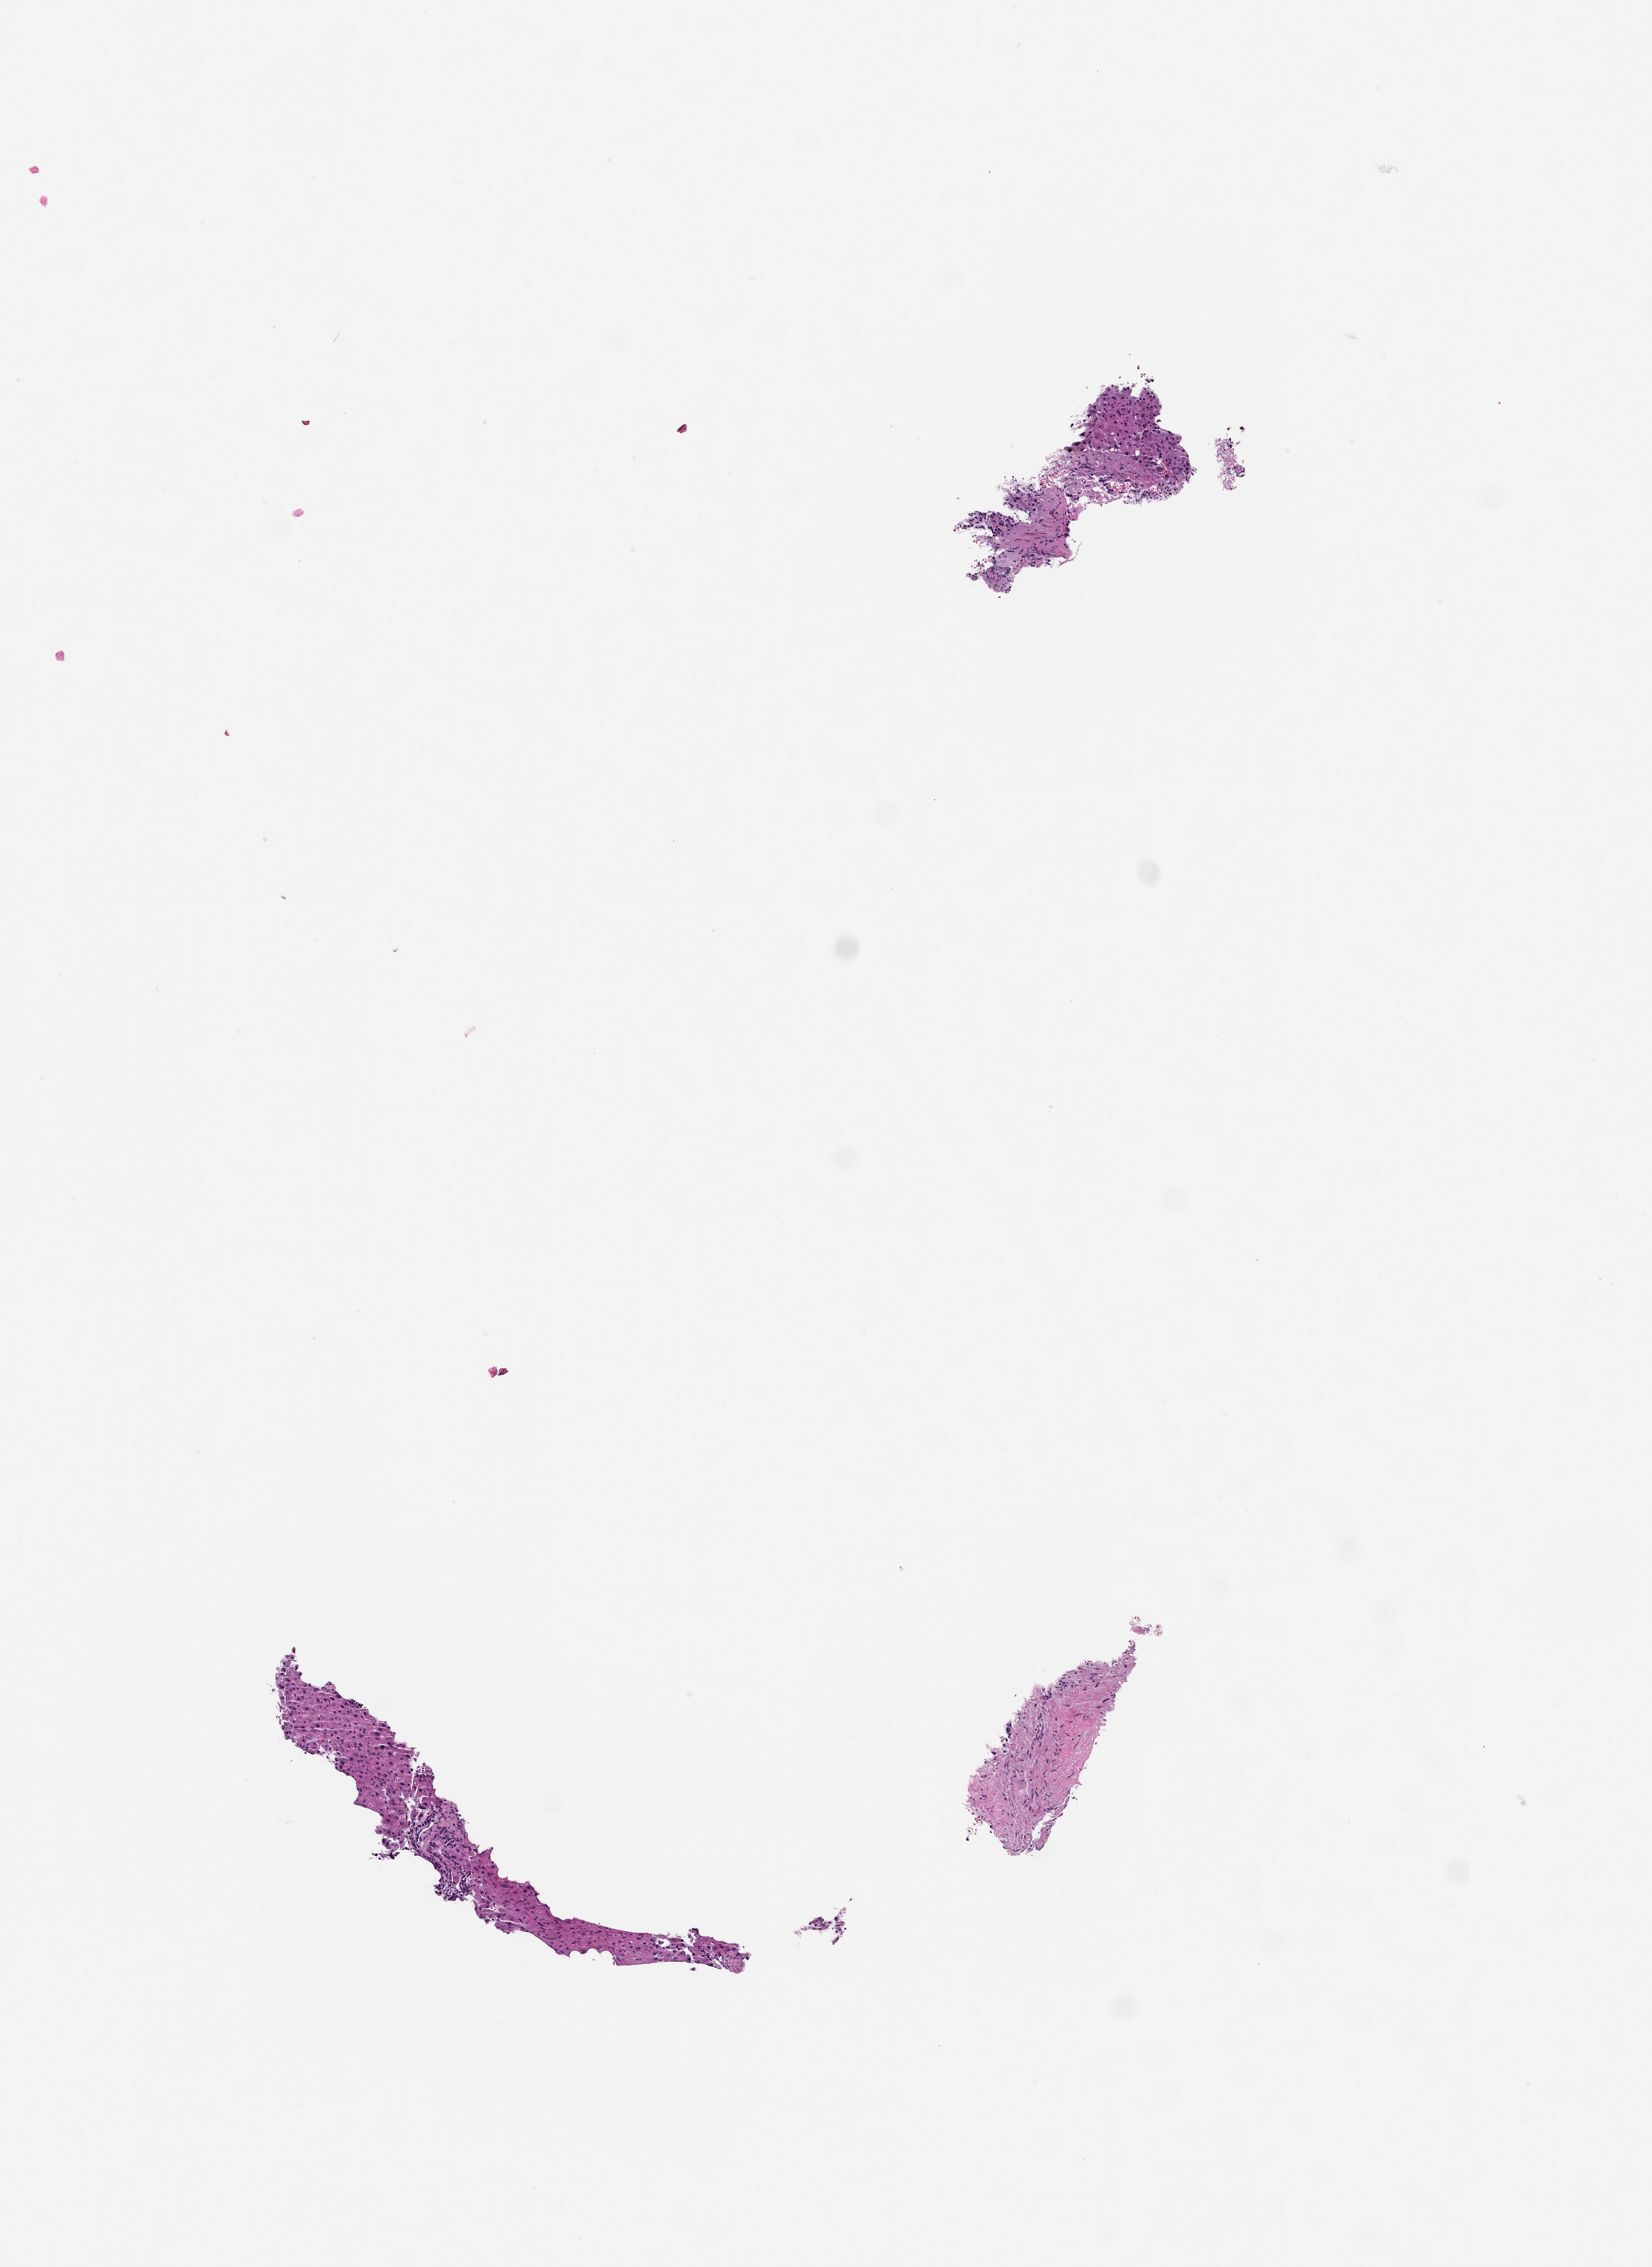
Hematoxylin and eosin (H&E) whole-slide image, whole scanned area (about 4.5 x 6.2 mm) shown as a low-resolution overview; FFPE section. Patient sex: female.
This section: metastatic tumor tissue. Patient diagnosis (primary): Invasive Breast Carcinoma.